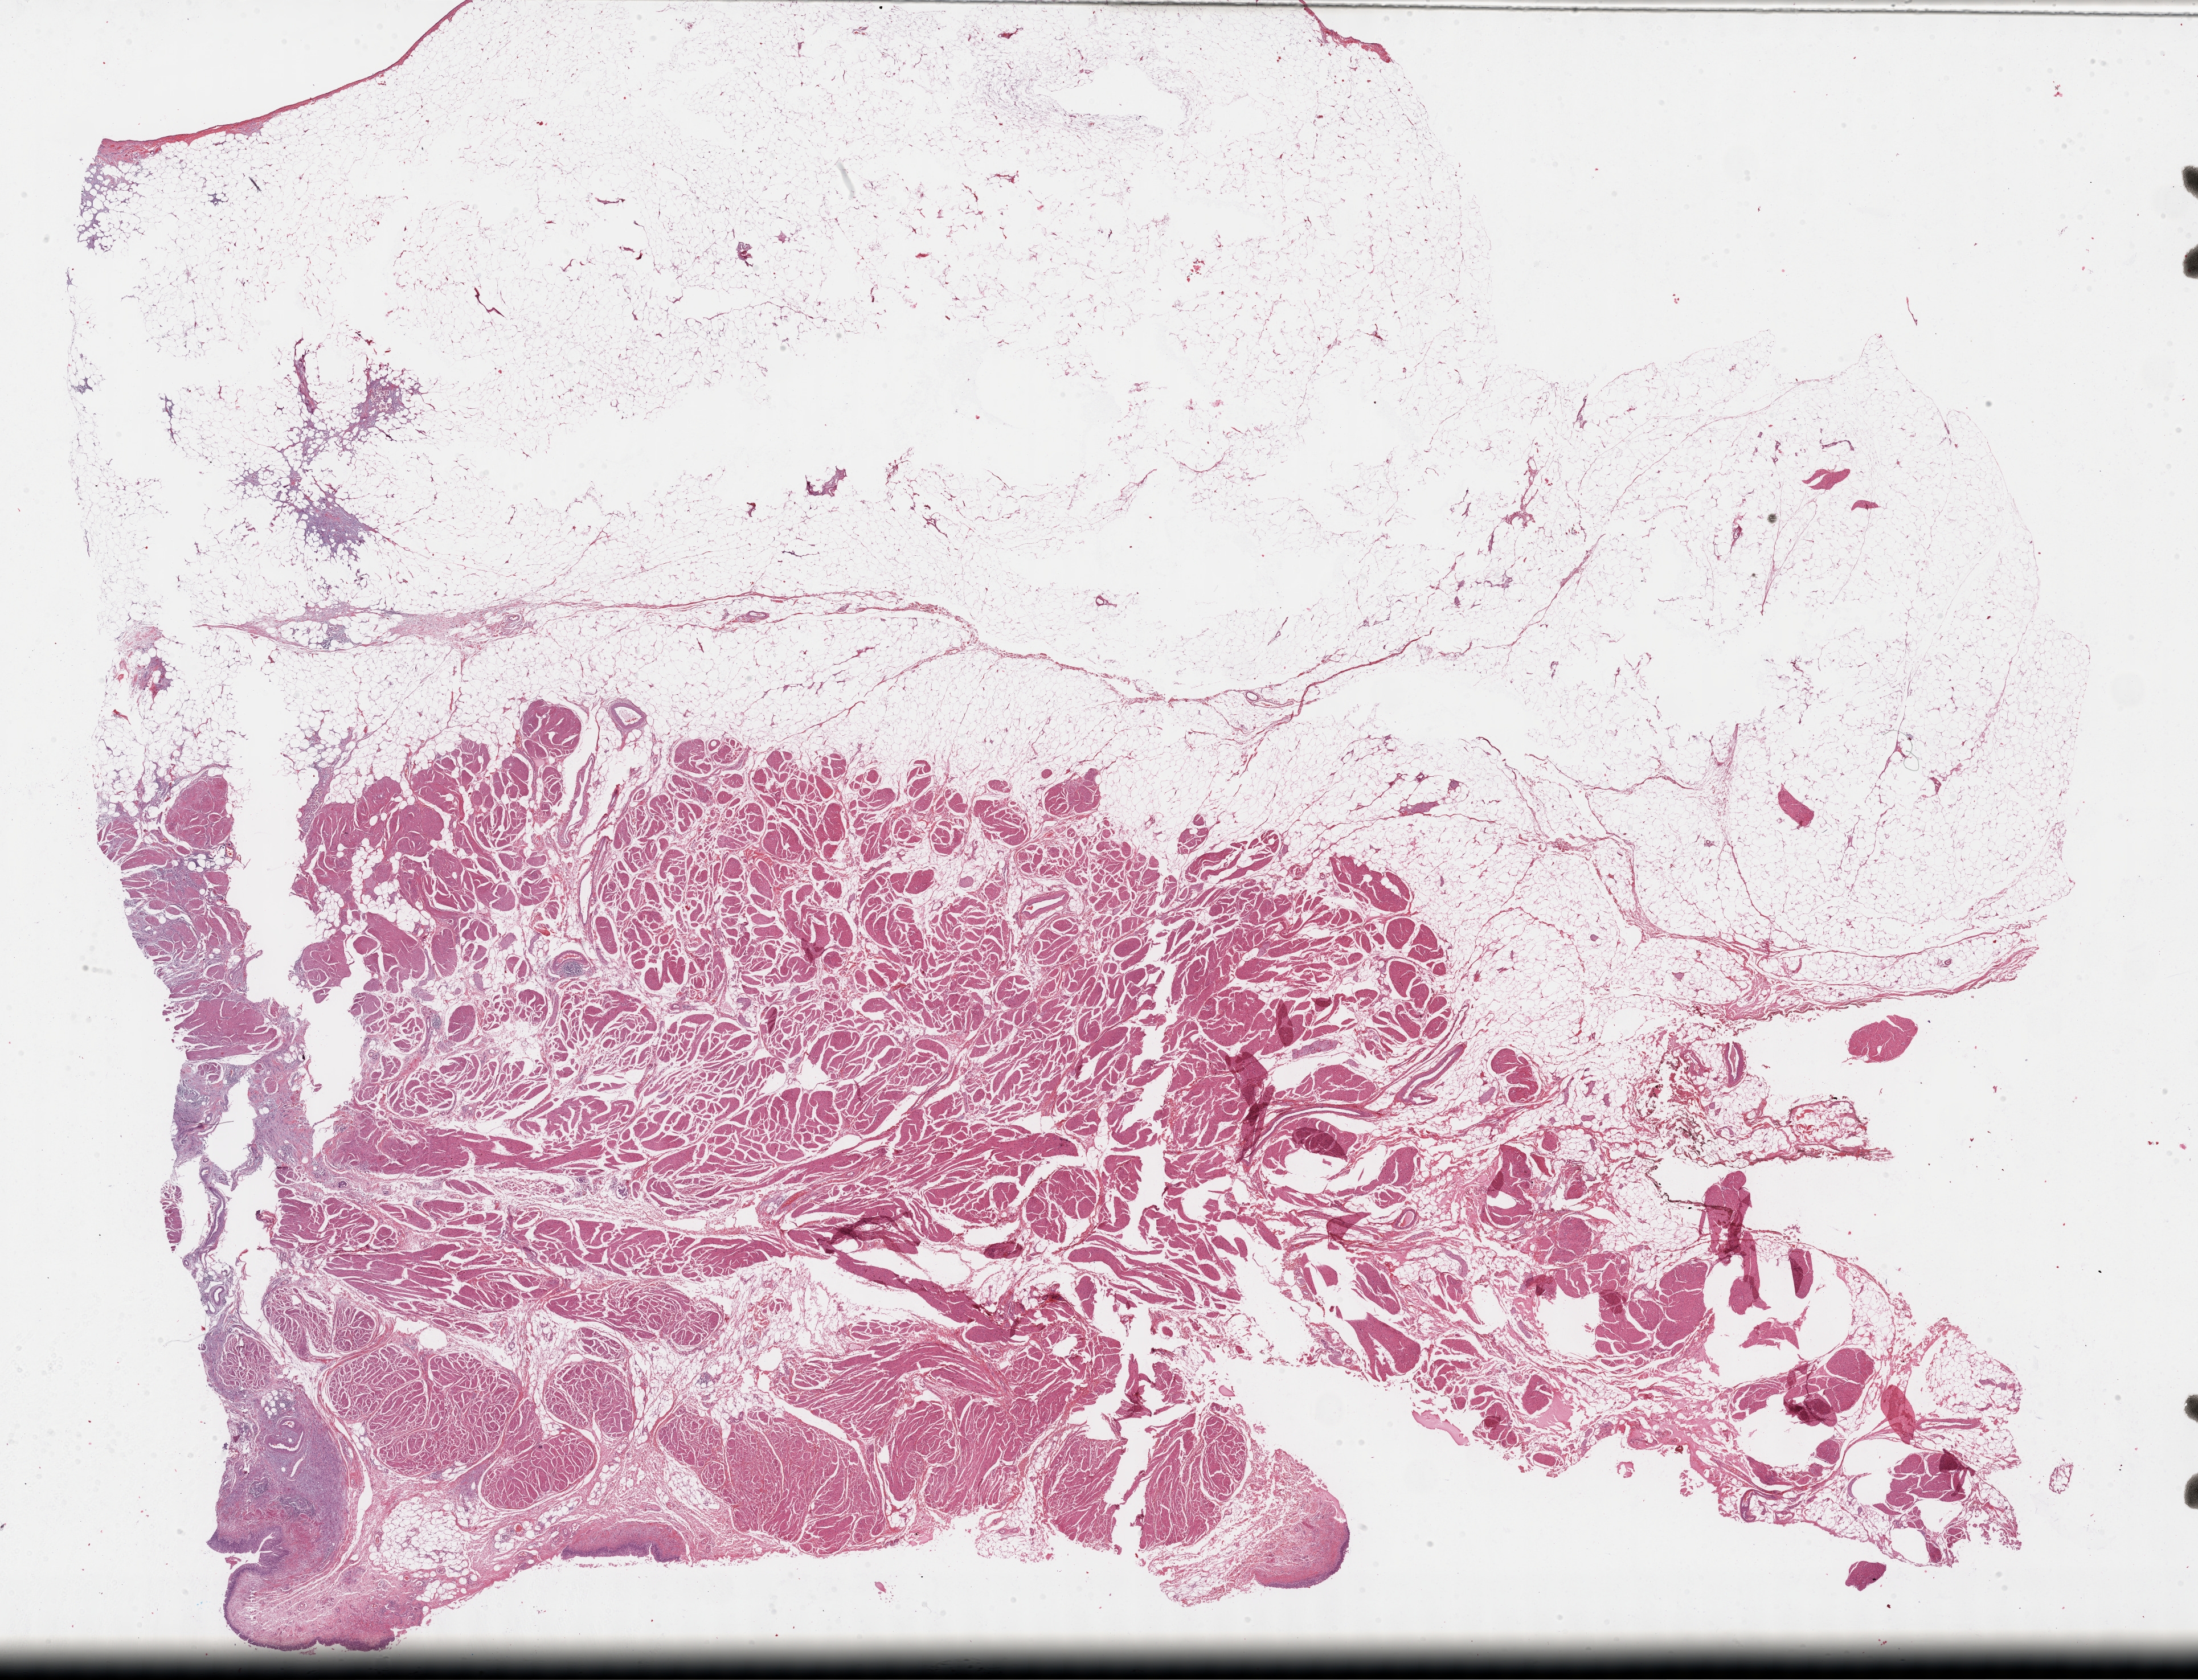
H&E whole-slide image — a low-resolution overview of the entire scanned area, about 31.2 x 23.9 mm. FFPE section. Sample: primary tumour, bladder. Male patient; age at initial diagnosis 69 years. Histologic grade: high grade.
* TNM: T3a N2 MX
* AJCC pathologic stage: IV (6th edition)
* diagnosis: Transitional cell carcinoma
* lymph nodes positive (case pathology): 6 of 60 examined